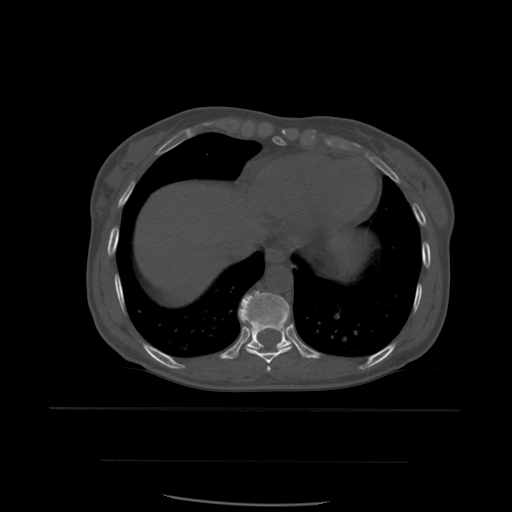
CT including the spine, one axial slice; position 327 of 574 along the scan axis; bone window (W 1800 / L 400 HU); 512 × 512 image matrix. Patient age 48 years. Case-level facts recorded for this patient, not image findings: primary cancer: lung; vertebrae with lytic lesions (as recorded): T11.
Annotated regions visible in this slice (semi-automatic segmentation, software-assisted and operator-edited):
- T10 vertebra: box from (x=239, y=291) to (x=291, y=350) px
- T8 vertebra: (x=267, y=366)–(x=271, y=372)
- T9 vertebra: (x=242, y=320)–(x=293, y=364)